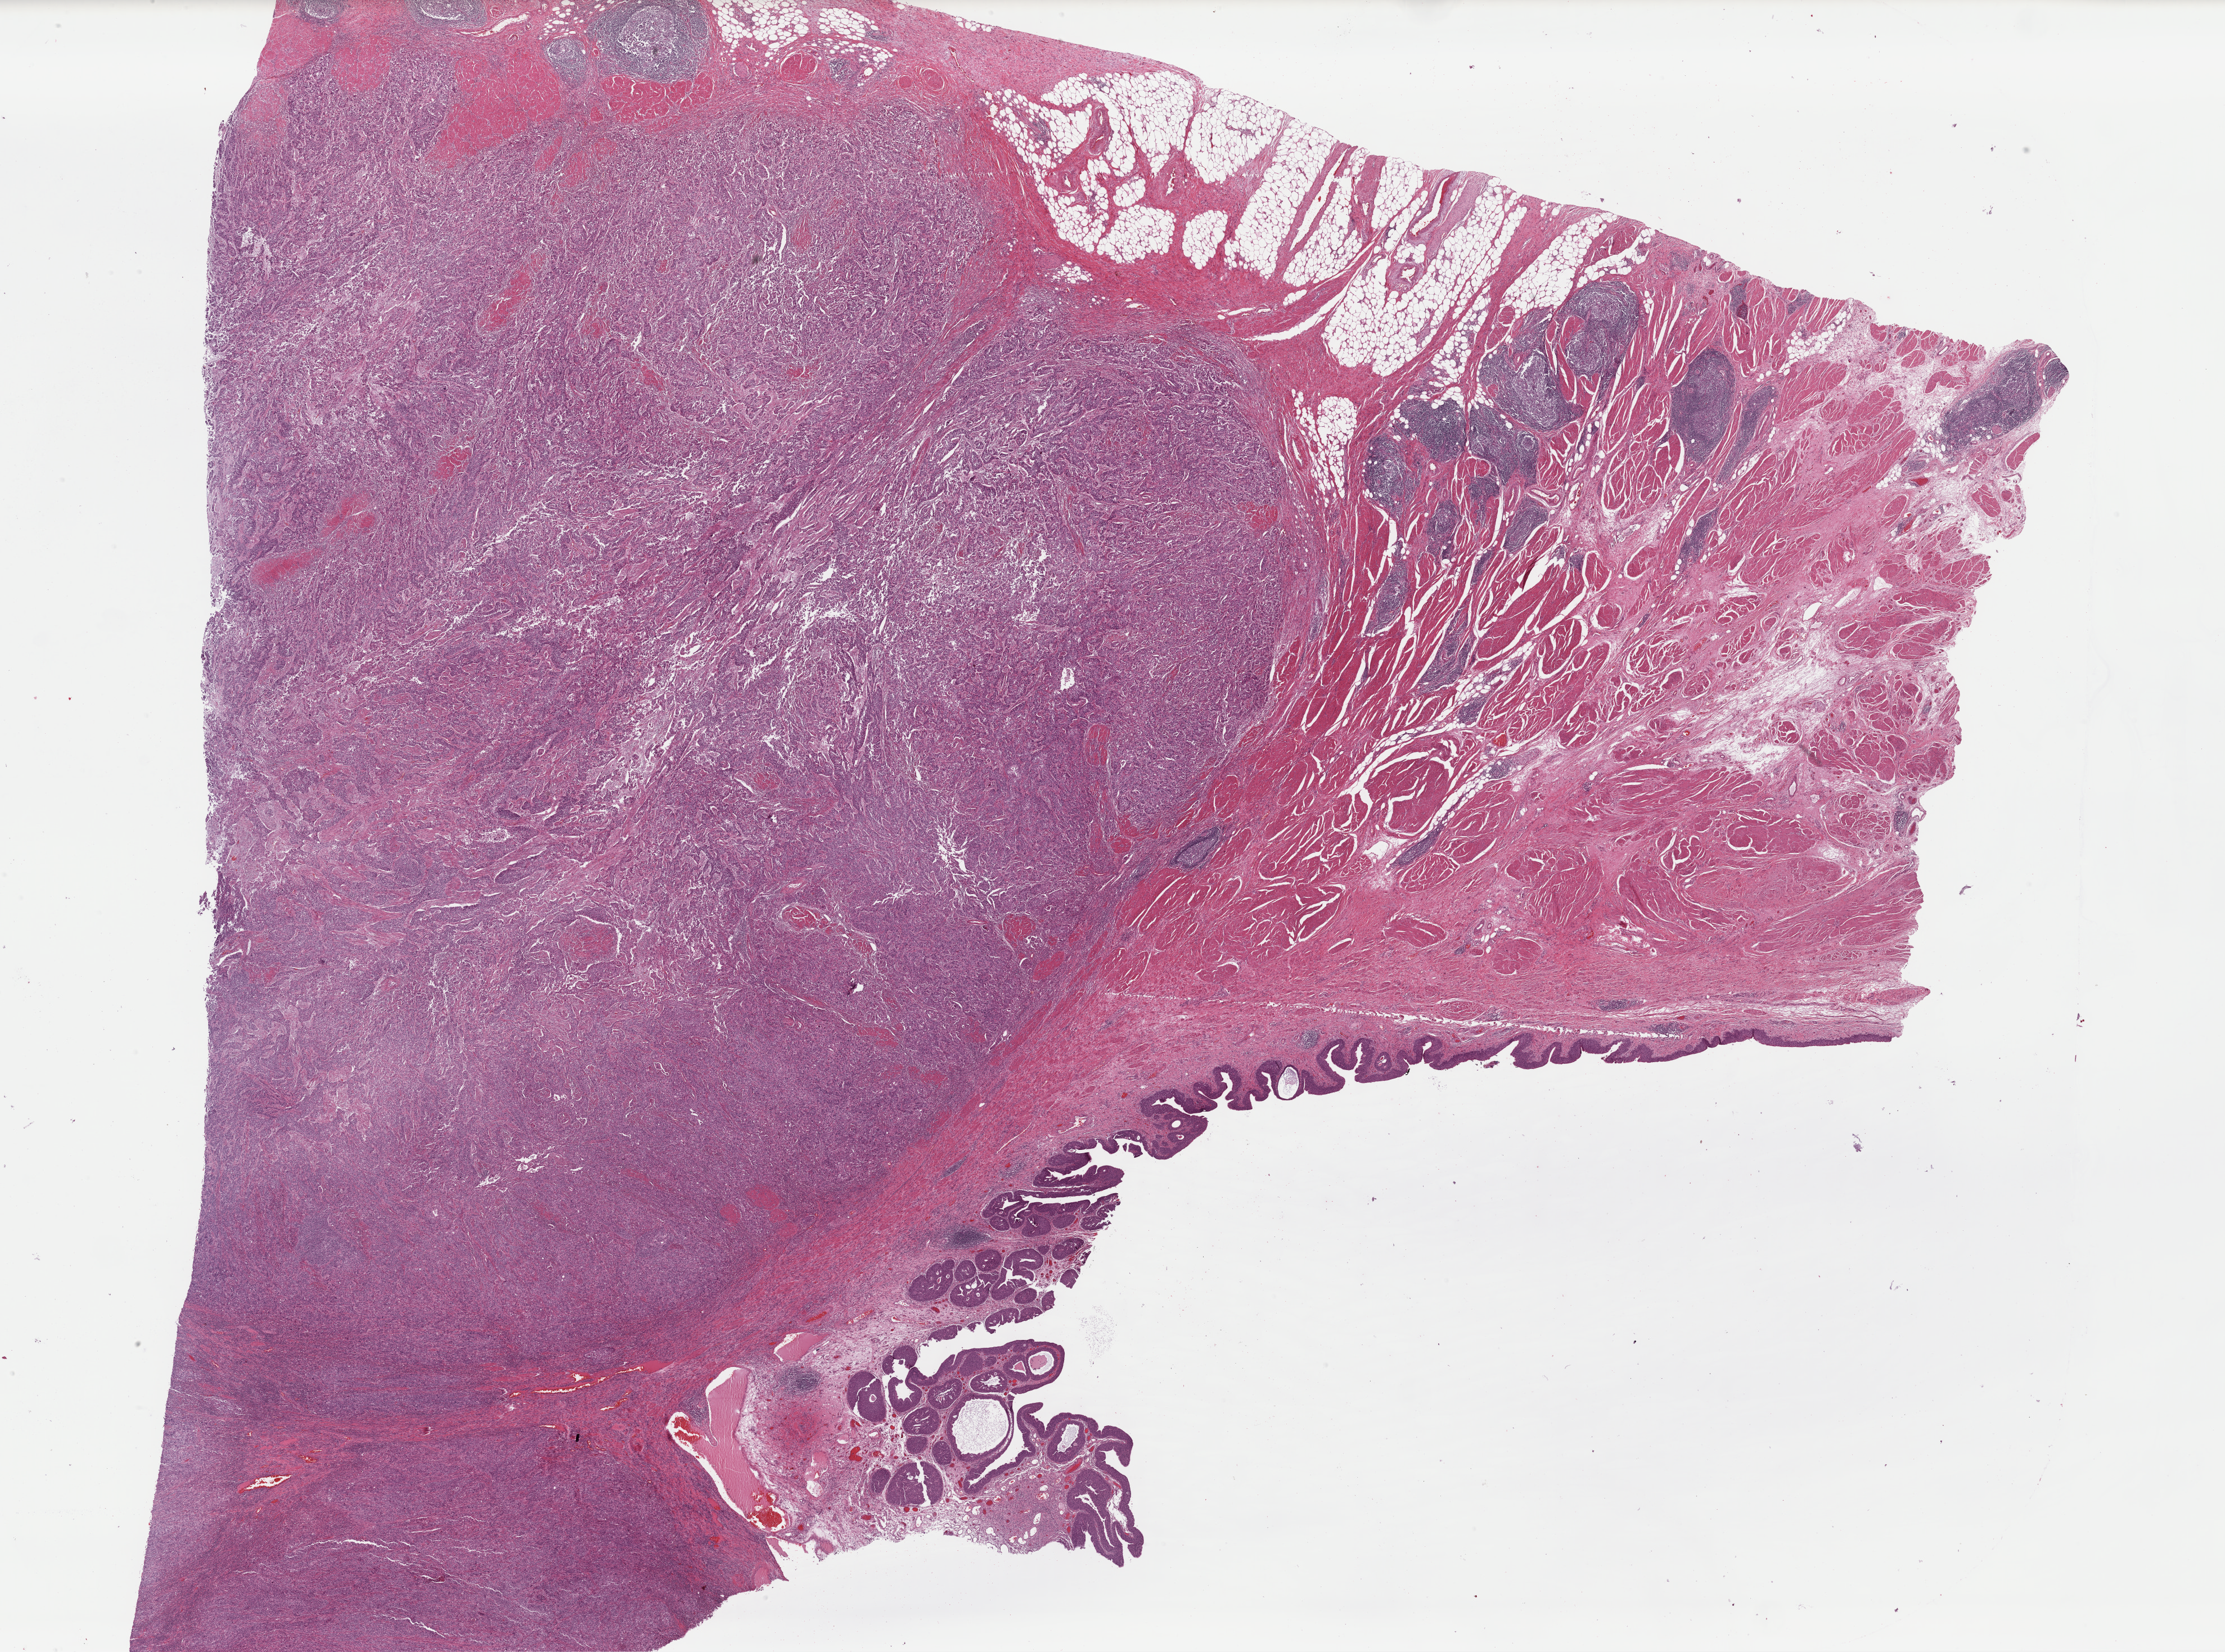
H&E whole-slide image, whole scanned area (about 31.2 x 23.2 mm, acquisition: 40x scan) shown as a low-resolution overview, formalin-fixed paraffin-embedded (FFPE) diagnostic section, bladder, primary tumour sample. Patient: male, age at initial diagnosis 60 years.
Diagnosis: Transitional cell carcinoma.